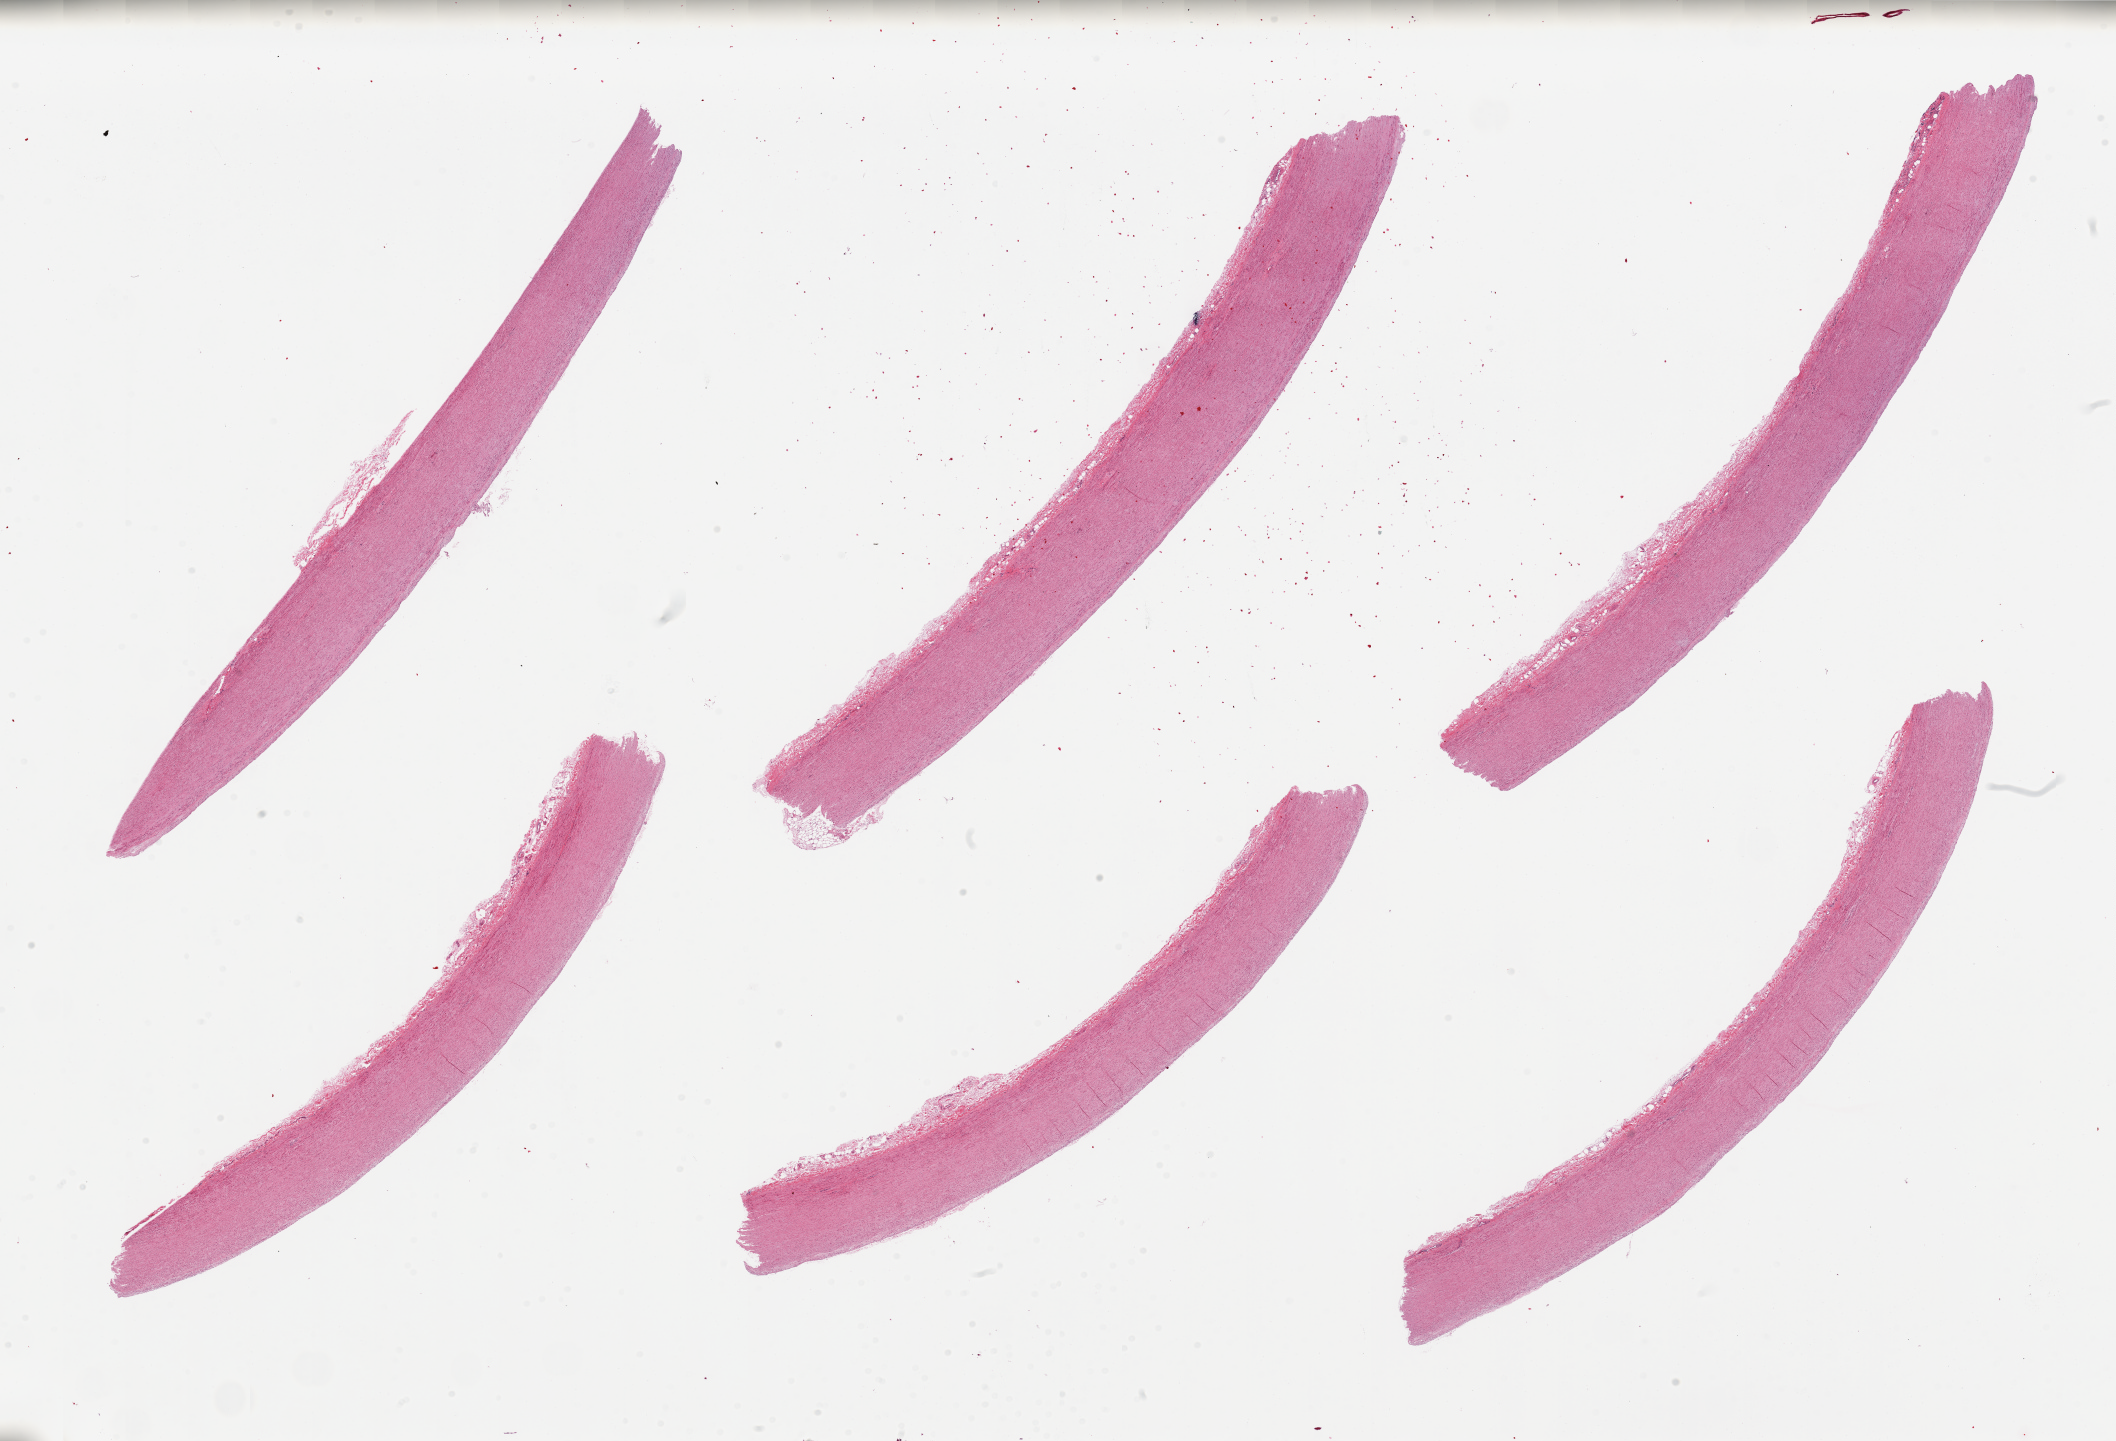
Digitized hematoxylin and eosin (H&E)-stained section, low-resolution overview of the scanned area, about 33.5 x 22.8 mm; PAXgene-fixed paraffin-embedded (PFPE) section; sampled site (target tissue): aorta; donor tissue sample. Male donor.
Review note (as recorded): 6 pieces; well trimmed.